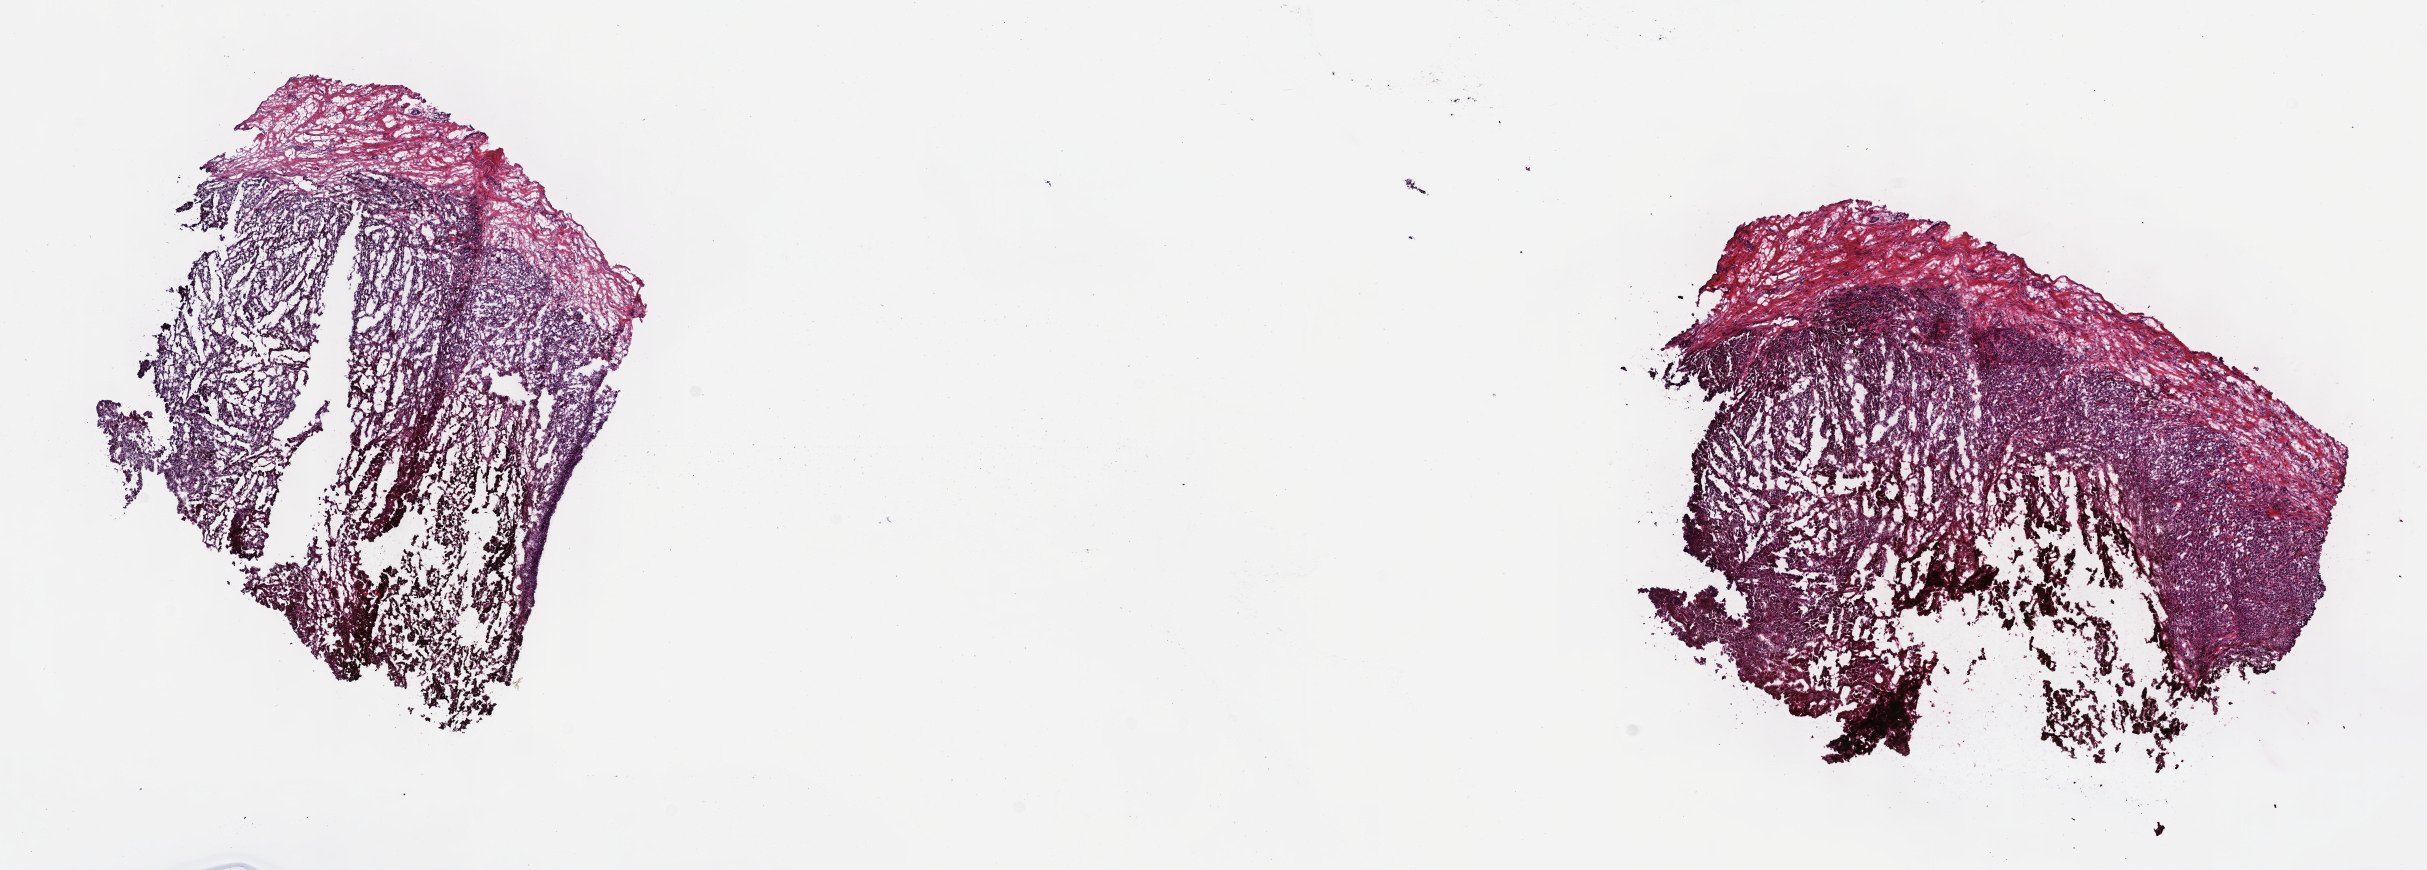
Whole-slide histology image, Hematoxylin and eosin (H&E) stained — shown as a low-resolution overview of the whole scanned area (about 19.6 x 7.0 mm); frozen section; metastatic tumour sample. Male patient; age at initial diagnosis 68 years. Composition of this section per pathologist review: tumour cells 75%, tumour nuclei 90%, normal cells 15%, stromal cells 10%, necrosis 0%. Infiltration values recorded for this section: lymphocyte infiltration 0%, monocyte infiltration 0%, neutrophil infiltration 0%.
This section: metastatic tumour tissue. Patient diagnosis: Malignant melanoma, NOS.